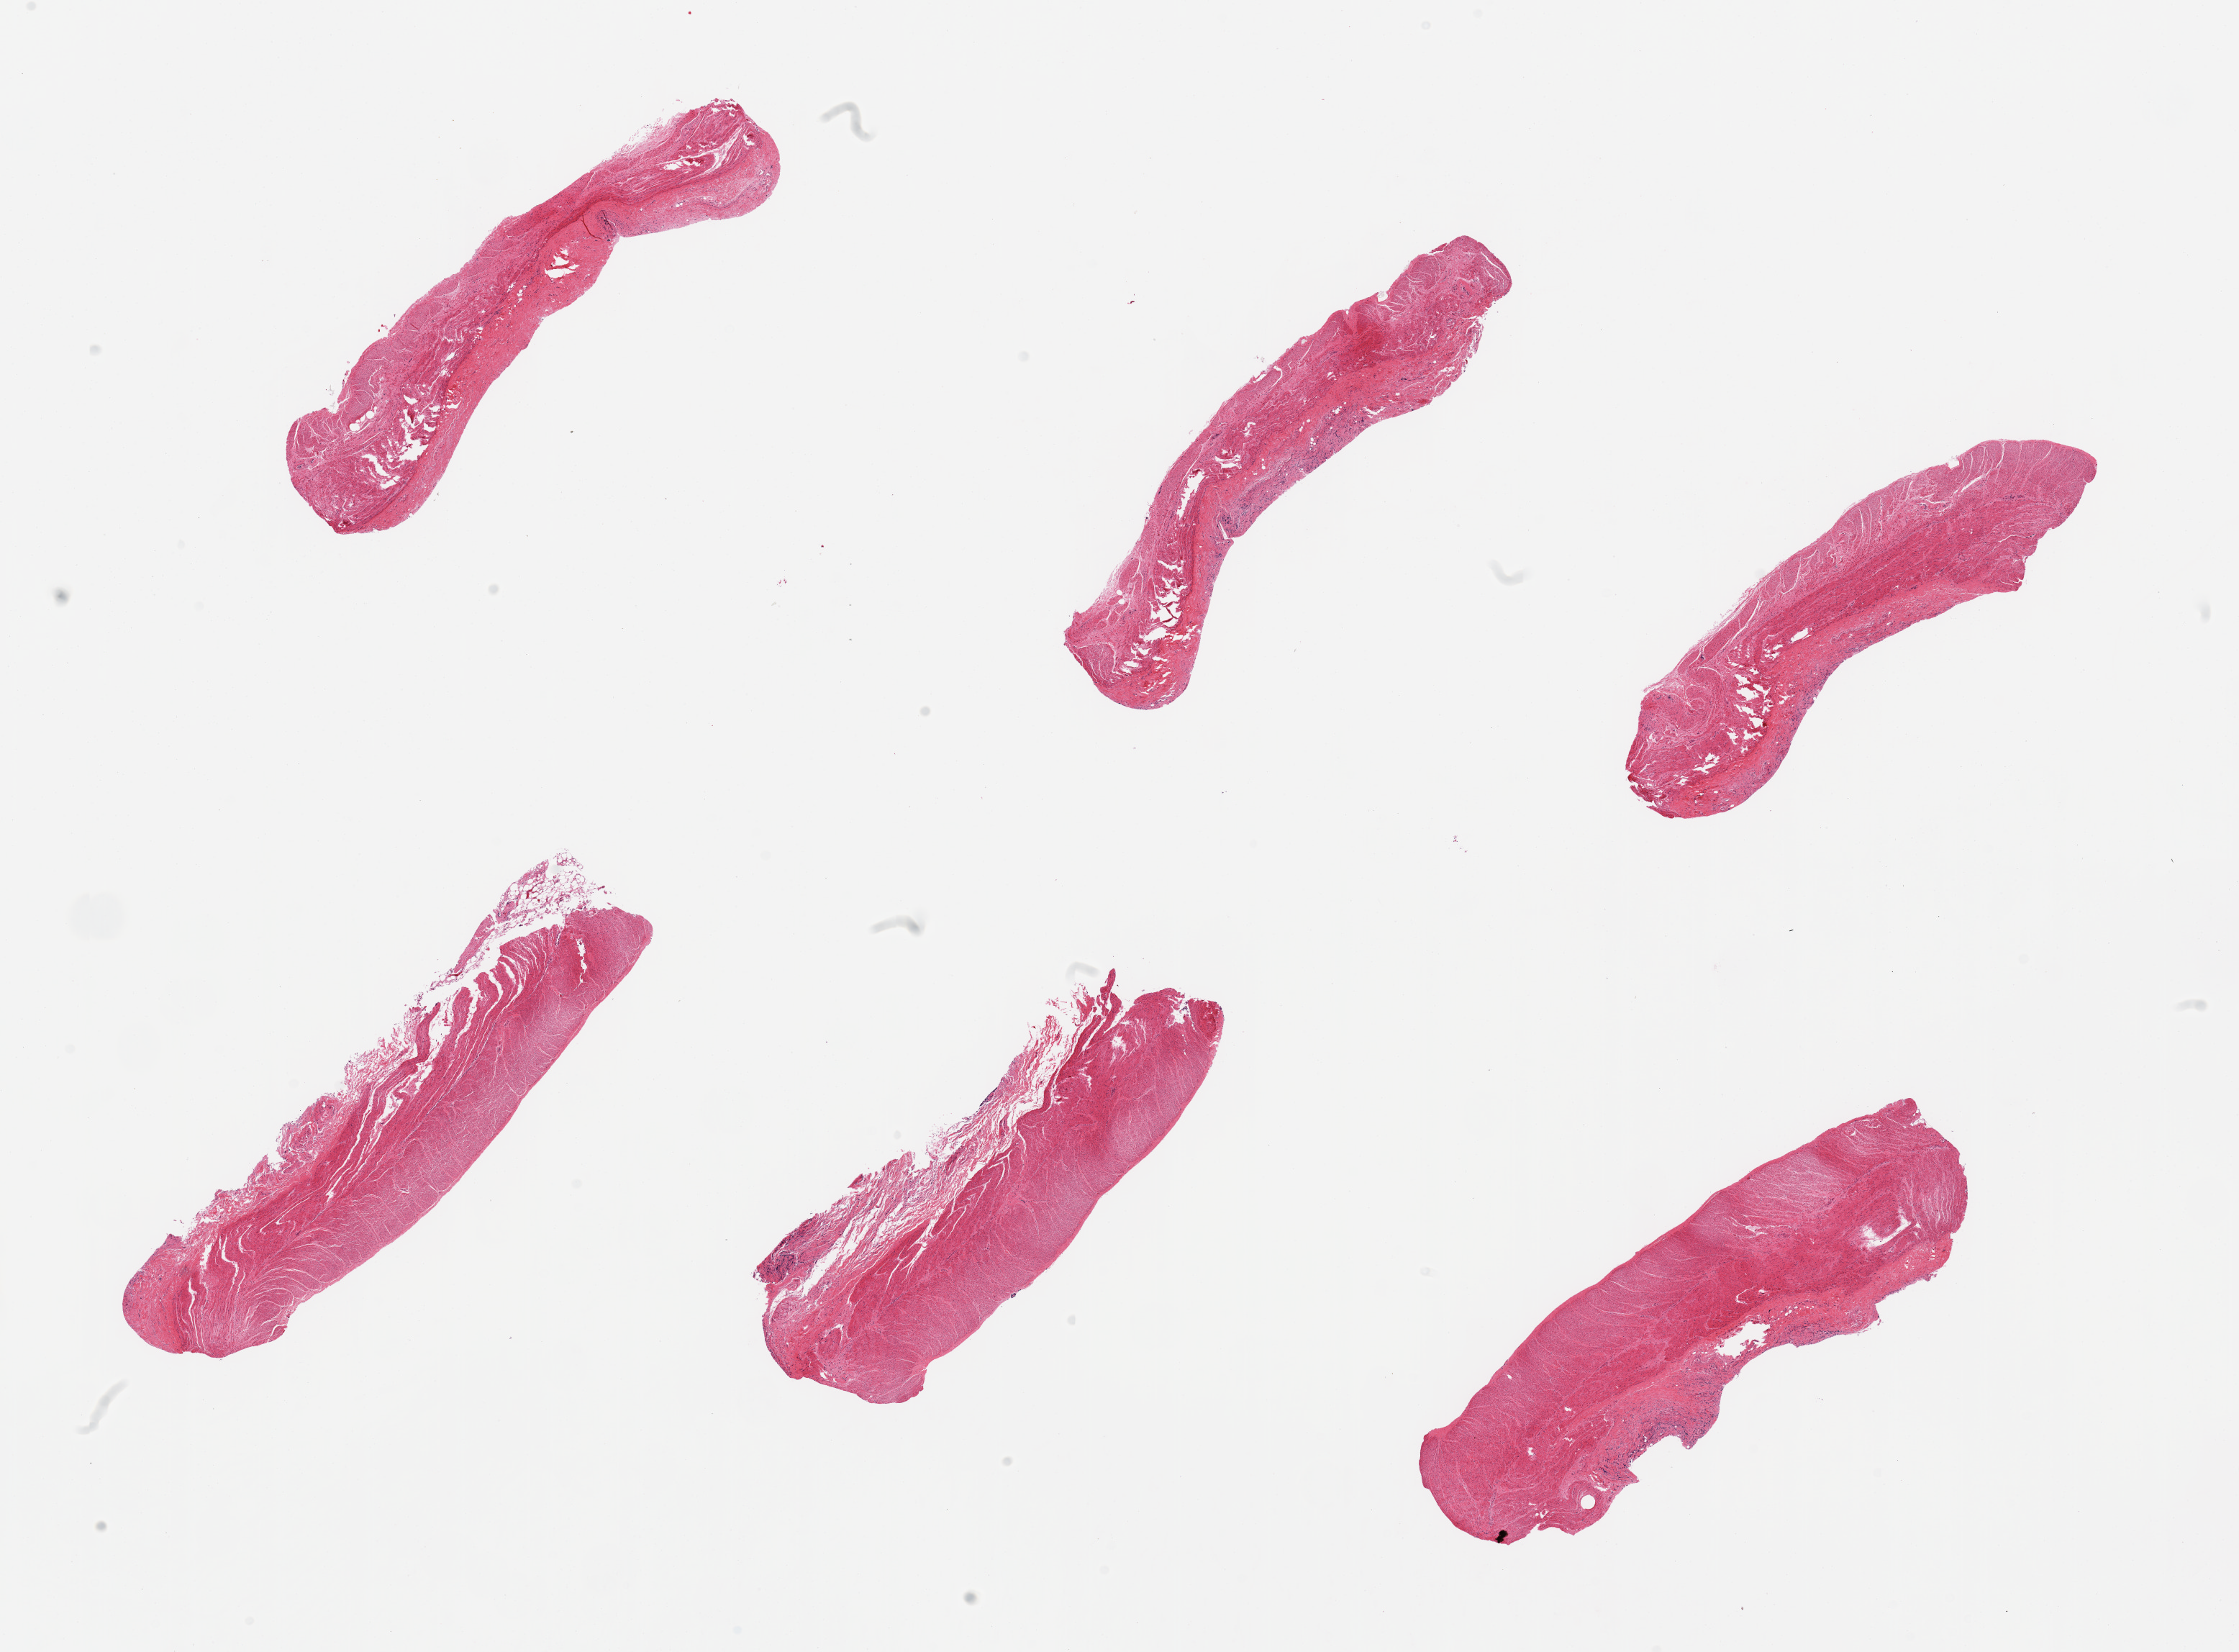
Hematoxylin and eosin (H&E) whole-slide image, a low-resolution overview of the entire scanned area, about 24.6 x 18.2 mm (slide scanned at 20x), PAXgene-fixed paraffin-embedded (PFPE) section, target tissue: sigmoid colon, tissue donor sample. Donor sex: male.
* review note (as recorded): 6 pieces, all muscularis